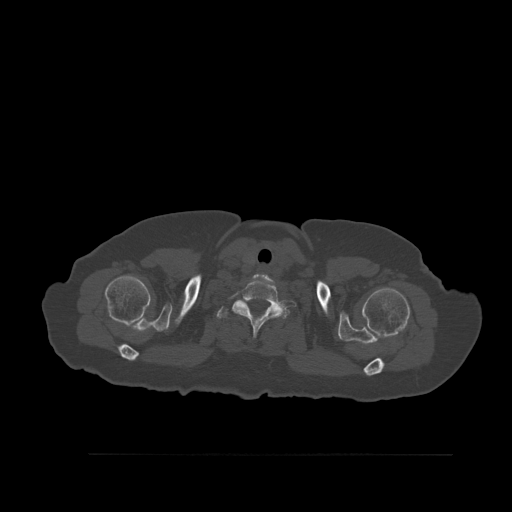
CT including the spine, one axial slice. Position 451 of 527 along the scan axis. Bone window (W 1800 / L 400 HU). 1.5 mm slice thickness. 512 × 512 image matrix, field of view 470 × 470 mm. Patient: female, 73 years. From the clinical record (not read from this slice): primary cancer: breast.
Annotated regions visible in this slice (semi-automatic segmentation, software-assisted and operator-edited):
- T1 vertebra: bounding box <216,306,287,319> (left, top, right, bottom; pixels)